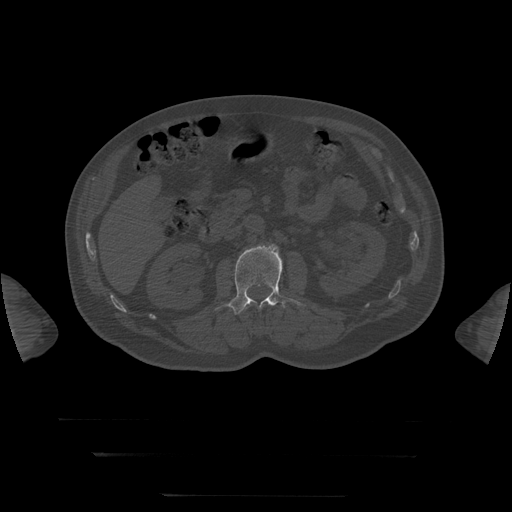
CT including the spine, one axial slice; position 25 of 397 along the scan axis; 120 kVp; bone window (W 1800 / L 400 HU); 512 × 512 image matrix, field of view 510 × 510 mm. Patient age 73 years. Case-level facts recorded for this patient, not image findings: primary cancer: prostate.
Annotated regions visible in this slice (semi-automatically segmented with operator editing):
- L1 vertebra: bounding box (x1, y1, x2, y2) in pixels: (247, 301, 269, 309)